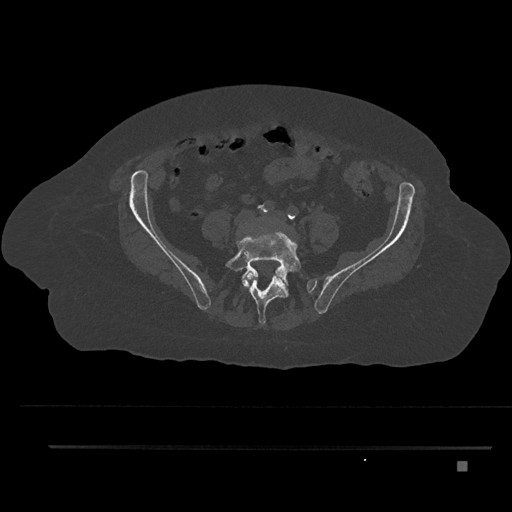
CT including the spine, one axial slice; reconstruction kernel Br40s/3; bone window (W 1800 / L 400 HU); 0.5 mm slice thickness; 512 × 512 image matrix, field of view 437 × 437 mm. Patient: female, 76 years. Case-level facts recorded for this patient, not image findings: primary cancer: lung; vertebrae with lytic lesions (as recorded): T11, L3.
Annotated regions visible in this slice (semi-automatically segmented with operator editing):
- L4 vertebra: box from (x=246, y=269) to (x=287, y=284) px
- L5 vertebra: (x=225, y=230)–(x=301, y=325)